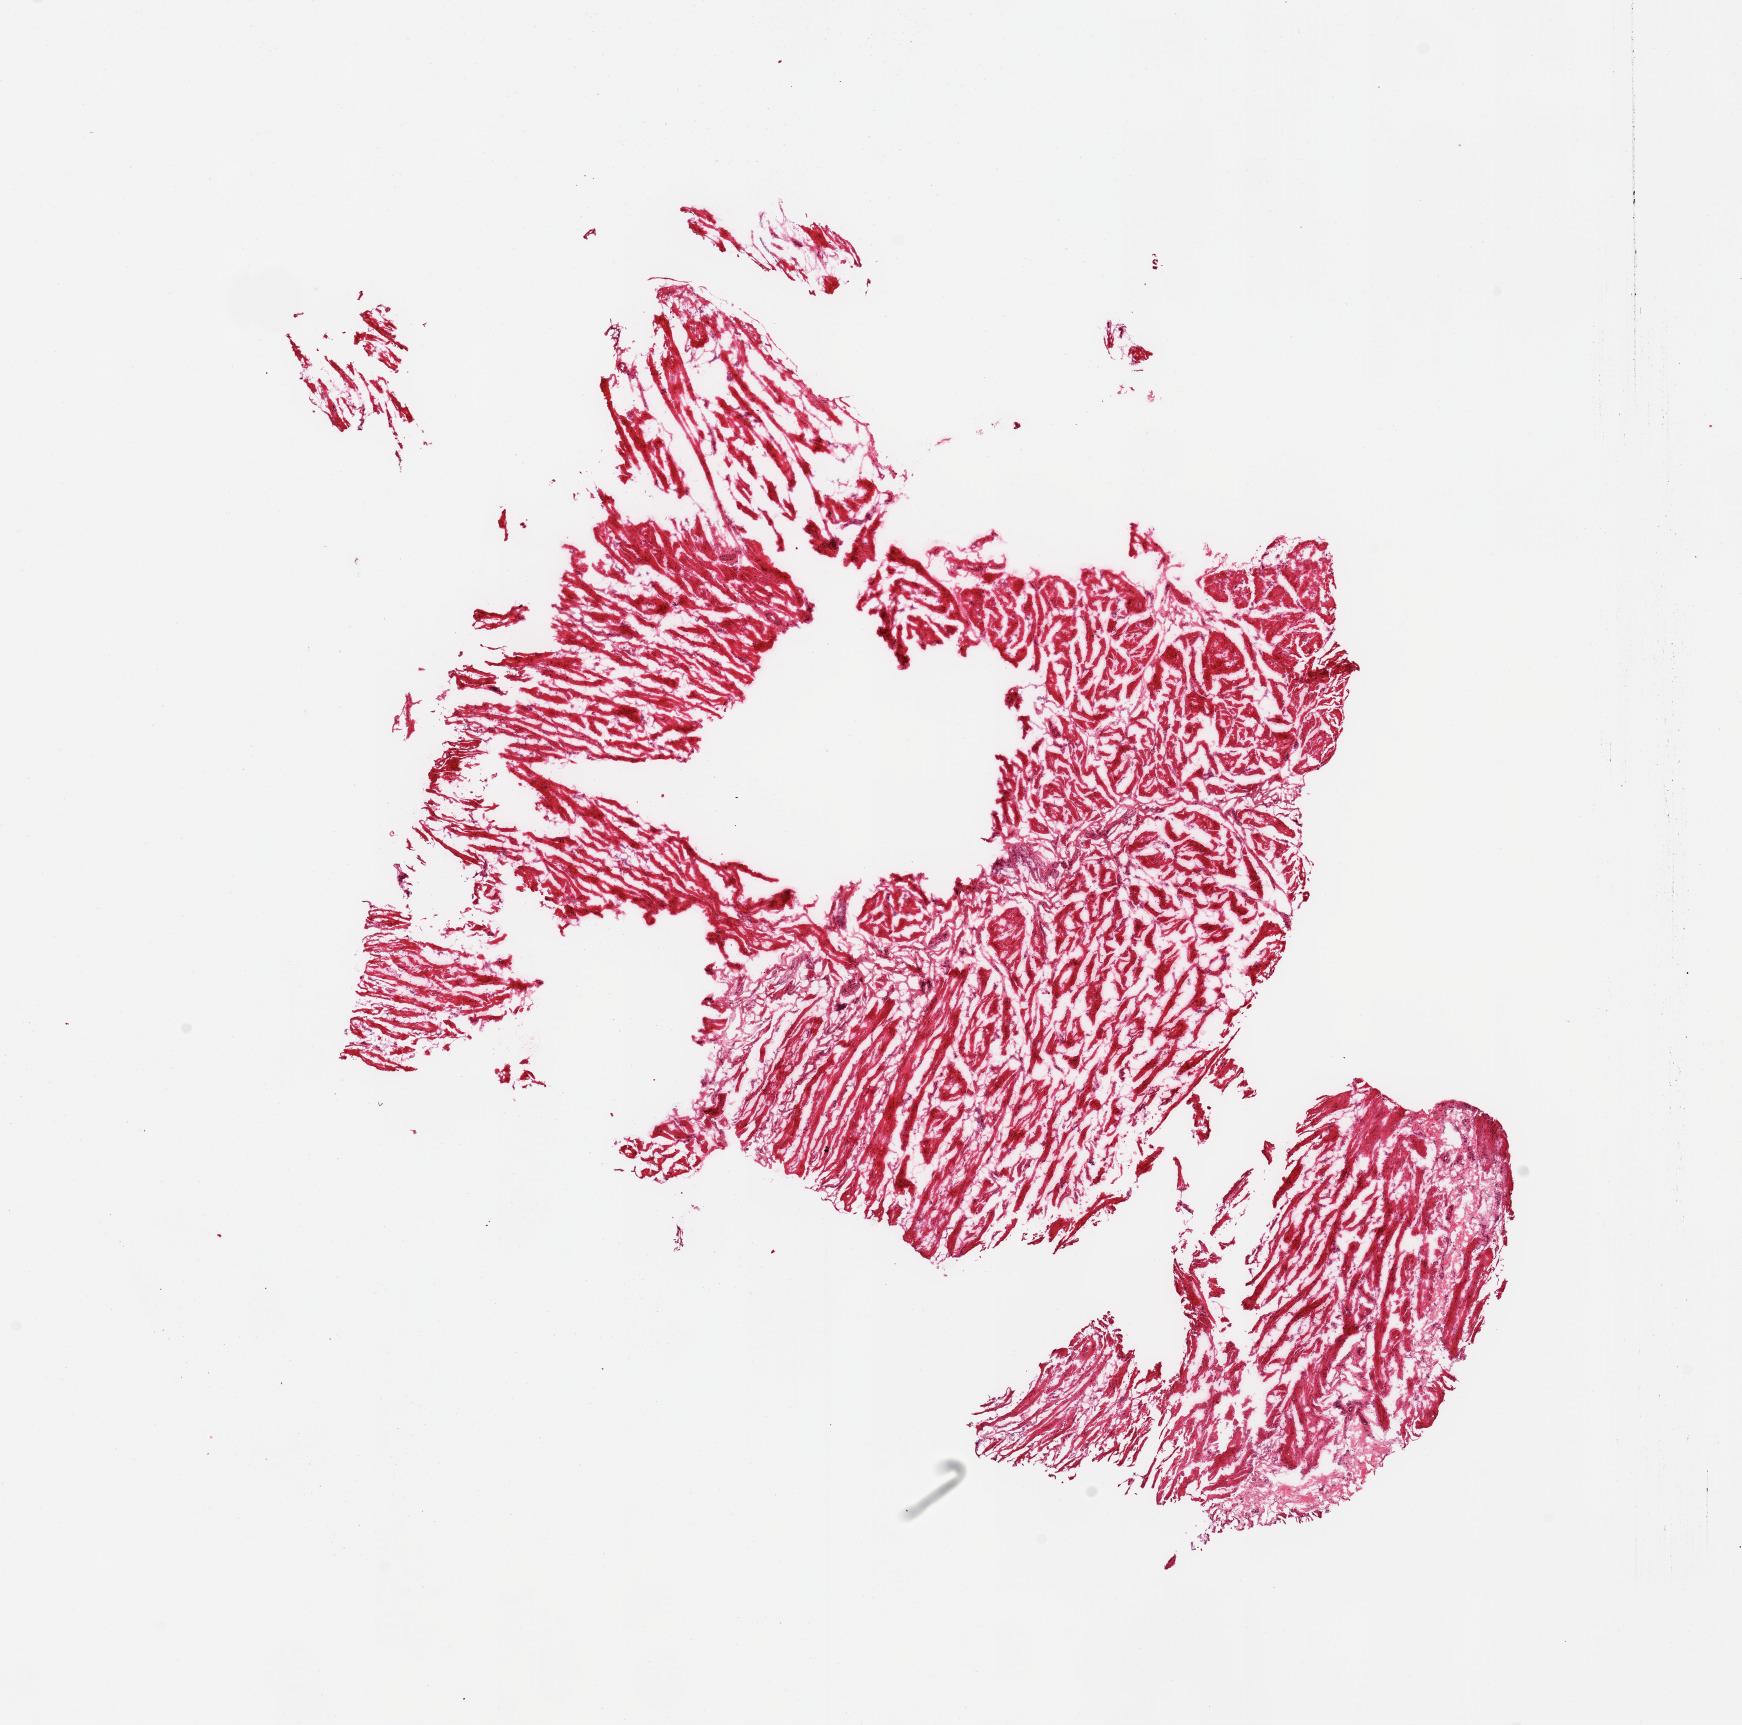
Digitized hematoxylin and eosin (H&E)-stained section, brightfield, low-resolution overview of the scanned area, about 13.8 x 13.6 mm.
Specimen: frozen section; target tissue: esophageal muscle; tissue donor sample.